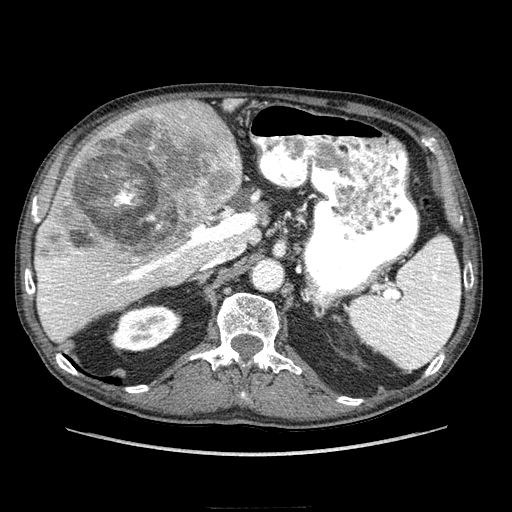
Contrast-enhanced abdominal CT (liver protocol), one axial slice. Position 147 of 218 along the scan axis. Reconstruction kernel STANDARD. 100 kVp. Soft-tissue window (W 400 / L 40 HU). 2.5 mm slice thickness. 512 × 512 image matrix, field of view 380 × 380 mm. Case-level facts recorded for this patient, not image findings: diagnosis: hepatocellular carcinoma (patient treated with transarterial chemoembolisation; whether this scan precedes or follows treatment is not stated here); TNM stage (as recorded): Stage-IIIA; Child-Pugh class: A; tumour differentiation: well differentiated; tumour nodularity: multinodular.
Structures marked on this image (semi-automatically segmented with operator editing):
- liver parenchyma outside the tumour (the mass and vessels are separate outlines, so this box may not span the whole liver): bounding box (x1, y1, x2, y2) in pixels: (34, 120, 266, 340)
- mass: (34, 99, 243, 277)
- liver vessels: (37, 194, 258, 329)